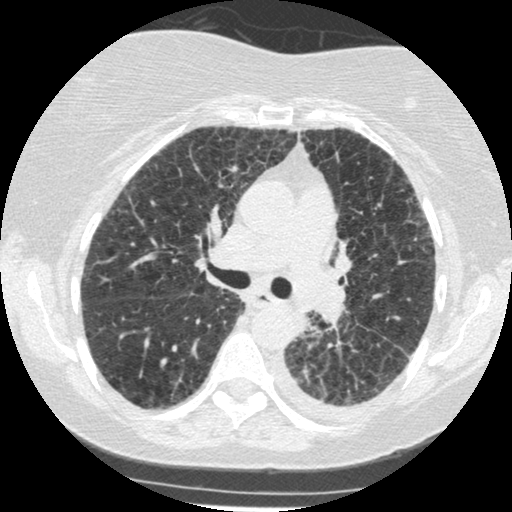
Low-dose screening chest CT, one axial slice; slice 168 of 341 in the series (ordered by position); reconstruction kernel STANDARD; 120 kVp; lung window (W 1500 / L -600 HU); 1.25 mm slice thickness; 512 × 512 image matrix, field of view 310 × 310 mm.
Annotated regions visible in this slice (manually delineated by an expert):
- lesion 1 (tumor, lower lobe of left lung): bounding box [x1, y1, x2, y2] px = [300, 314, 309, 331]